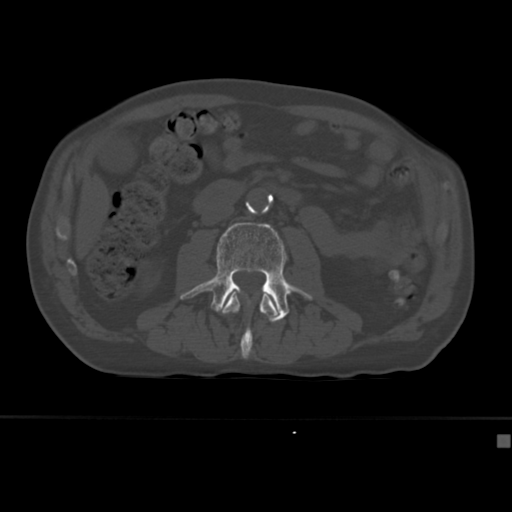
CT including the spine, one axial slice. Slice 134 of 430 in the series (ordered by position). Reconstruction kernel Br40s. 120 kVp. Bone window (W 1800 / L 400 HU). 512 × 512 image matrix, field of view 337 × 337 mm. Patient: male, 64 years. Case-level facts recorded for this patient, not image findings: primary cancer: uterus; vertebrae with lytic lesions (as recorded): T1, T4, T5, T7, L5.
Structures marked on this image (semi-automatic segmentation, software-assisted and operator-edited):
- L2 vertebra: bounding box <221,291,280,359> (left, top, right, bottom; pixels)
- L3 vertebra: <180,222,313,323>